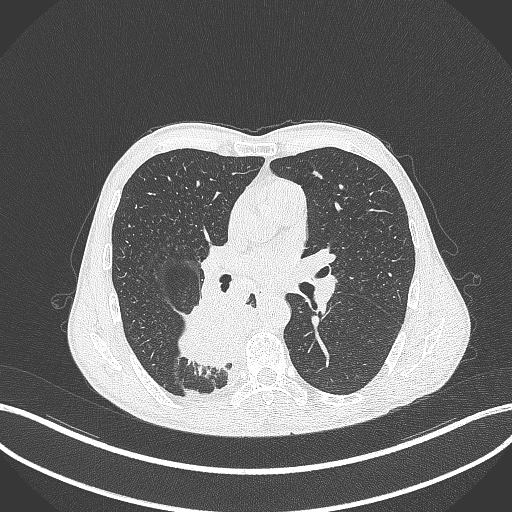
Chest CT, one axial slice; slice 204 of 371 in the series (ordered by position); 120 kVp; lung window (W 1500 / L -600 HU); 512 × 512 image matrix. Male patient, age 58 years. Case-level facts recorded for this patient, not image findings: clinical TNM (as recorded): T3 N1 M1.
Outlined on this slice (rectangle marked by the reading radiologist):
- lung tumour (recorded histology: squamous cell carcinoma): bounding box <172,296,257,371> (left, top, right, bottom; pixels)